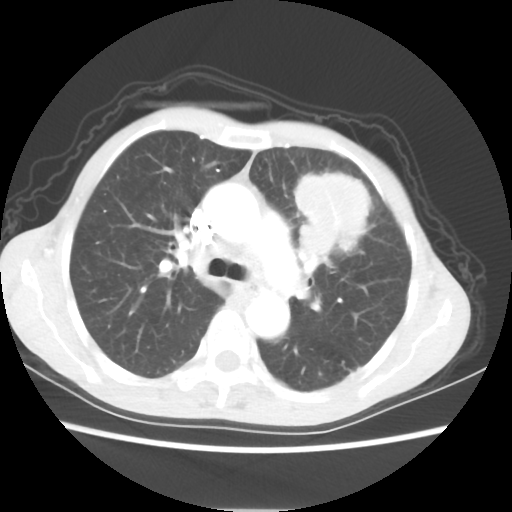
Chest CT, one axial slice. Position 38 of 56 along the scan axis. Reconstruction kernel STANDARD. 80 kVp. Lung window (W 1500 / L -600 HU). 512 × 512 image matrix, field of view 331 × 331 mm. Patient: female, 60 years. From the clinical record (not read from this slice): clinical TNM (as recorded): T4 N1 M0.
Outlined on this slice (rectangle marked by the reading radiologist):
- lung tumour (recorded histology: adenocarcinoma): bounding box <292,170,372,271> (left, top, right, bottom; pixels)